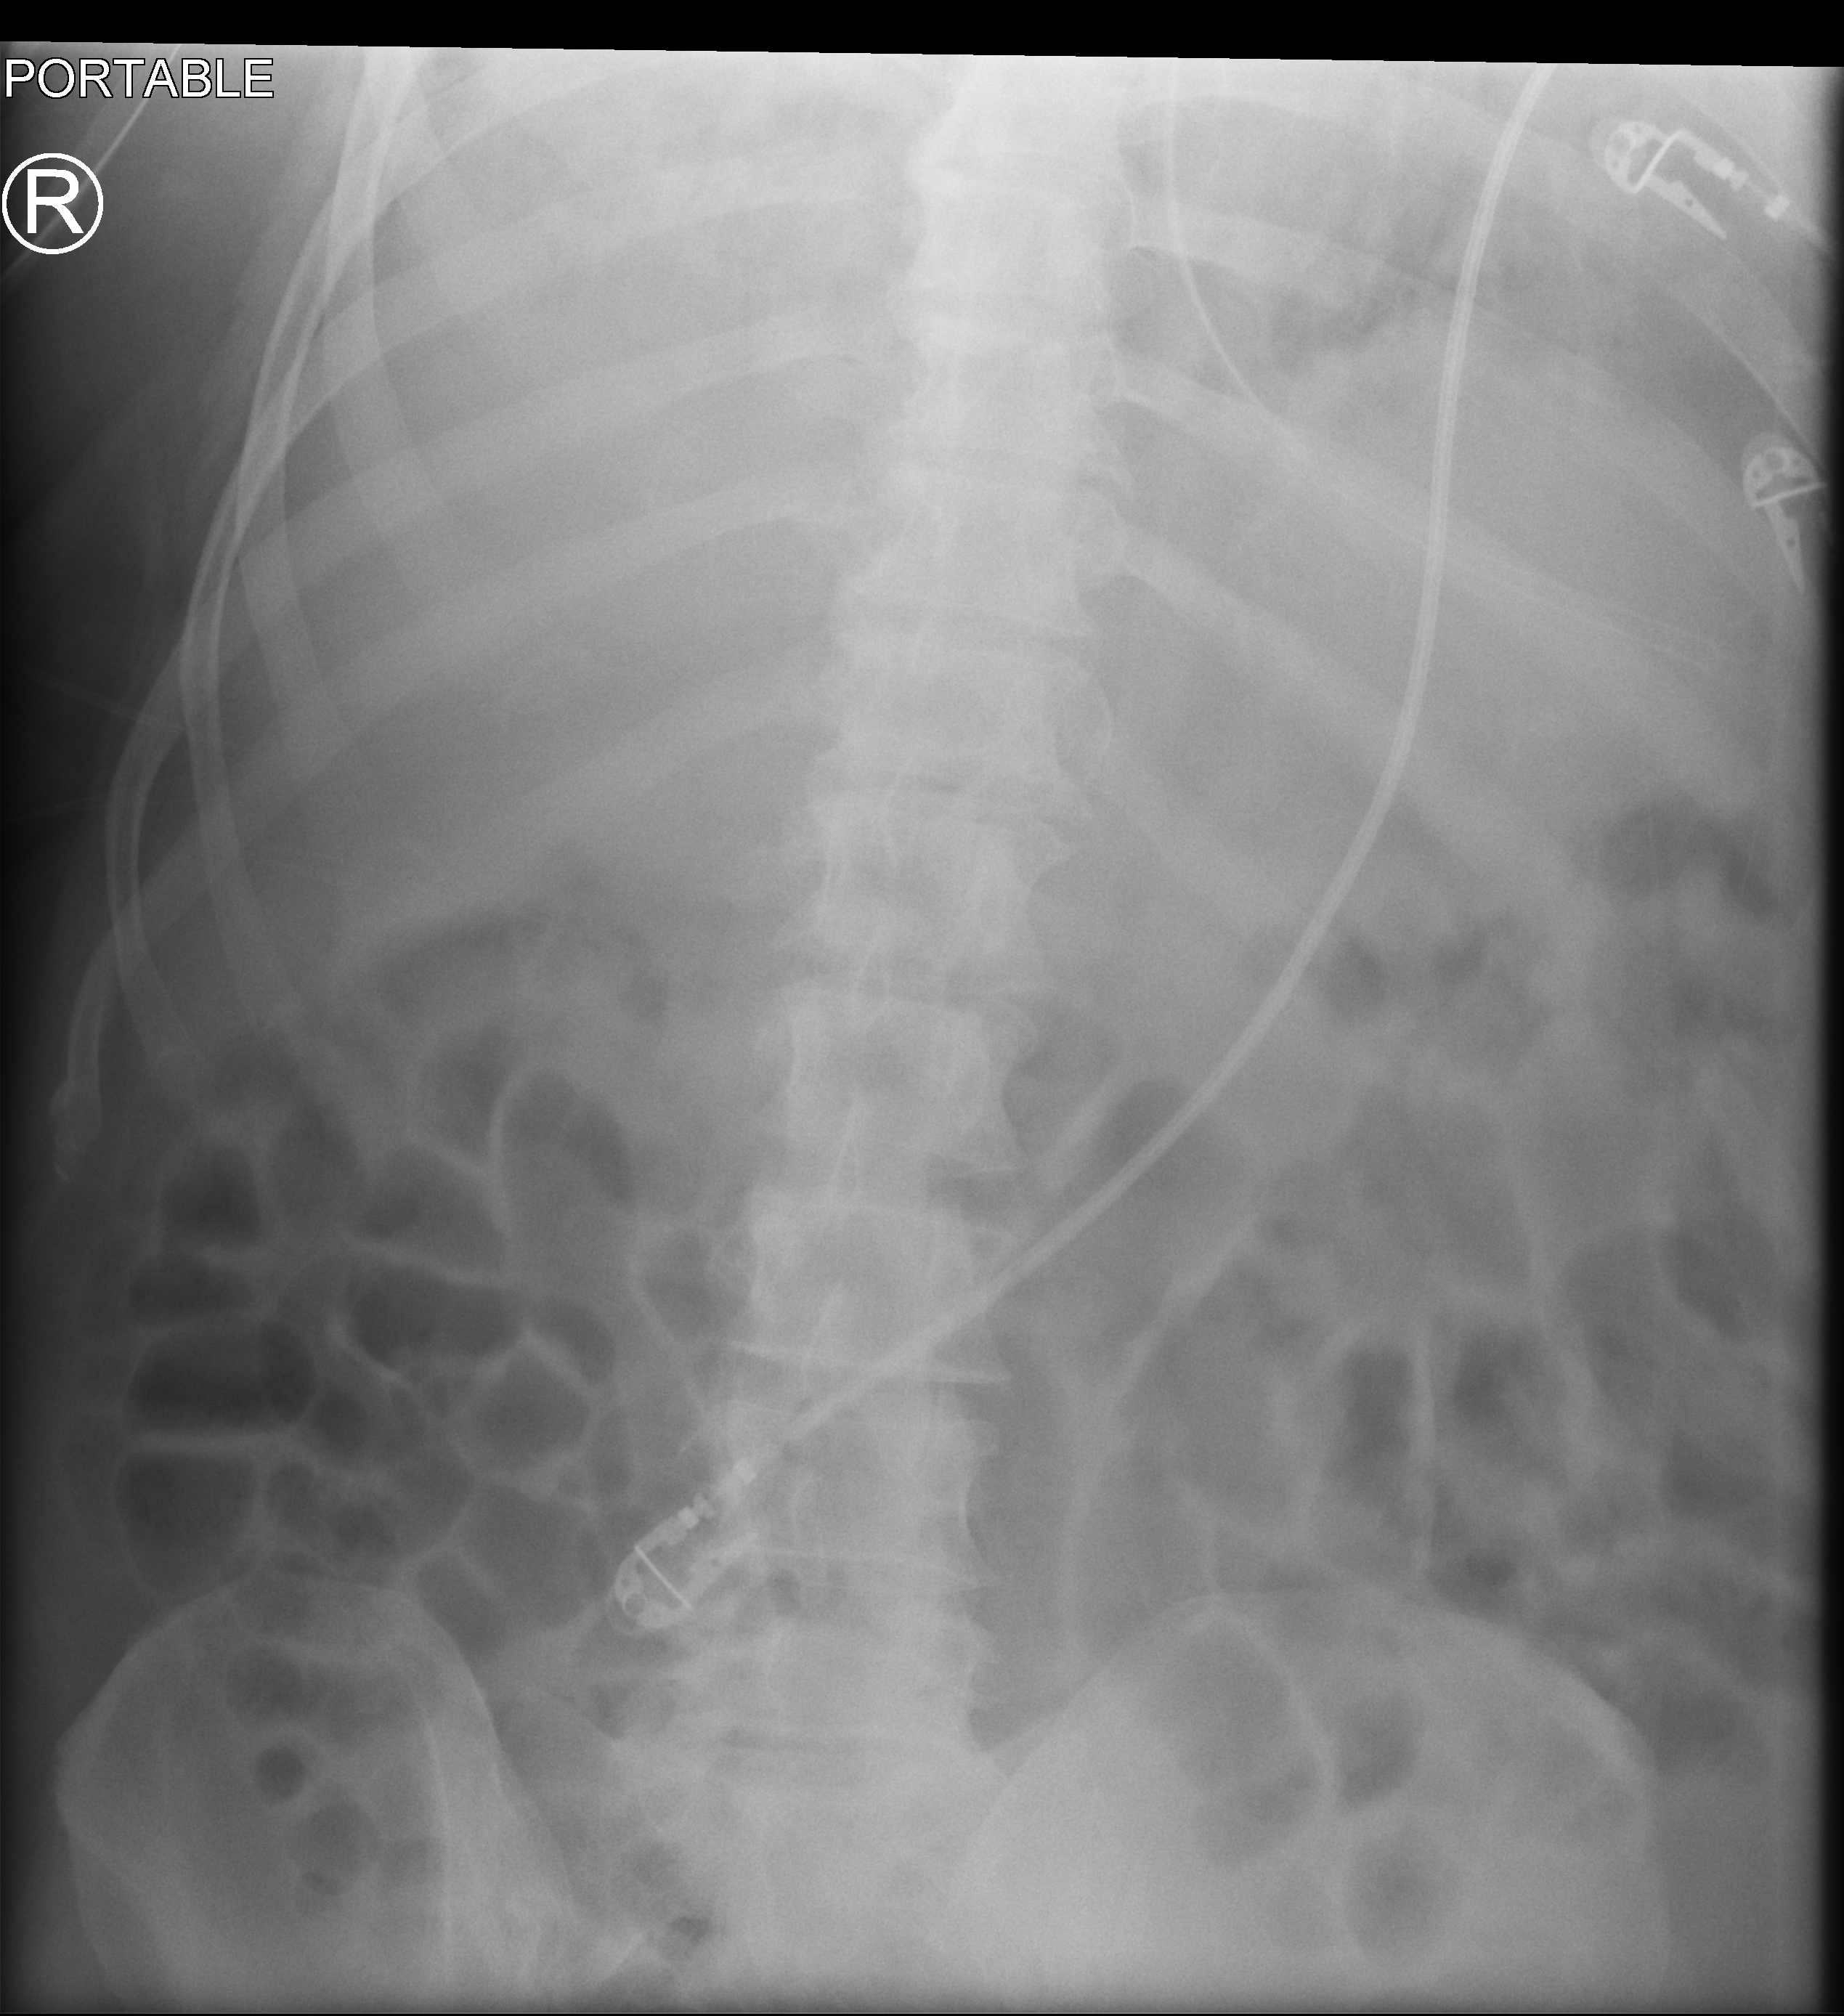
Portable abdomen radiograph; anteroposterior (AP) projection. Patient hospitalised with COVID-19; male, aged 60–74 years.
Hospital-stay facts (about this admission, not read from this image; timing relative to this image not recorded):
- admitted to intensive care during this hospital stay: yes
- chronic kidney disease (admission record): no
- mechanically ventilated during this hospital stay: yes